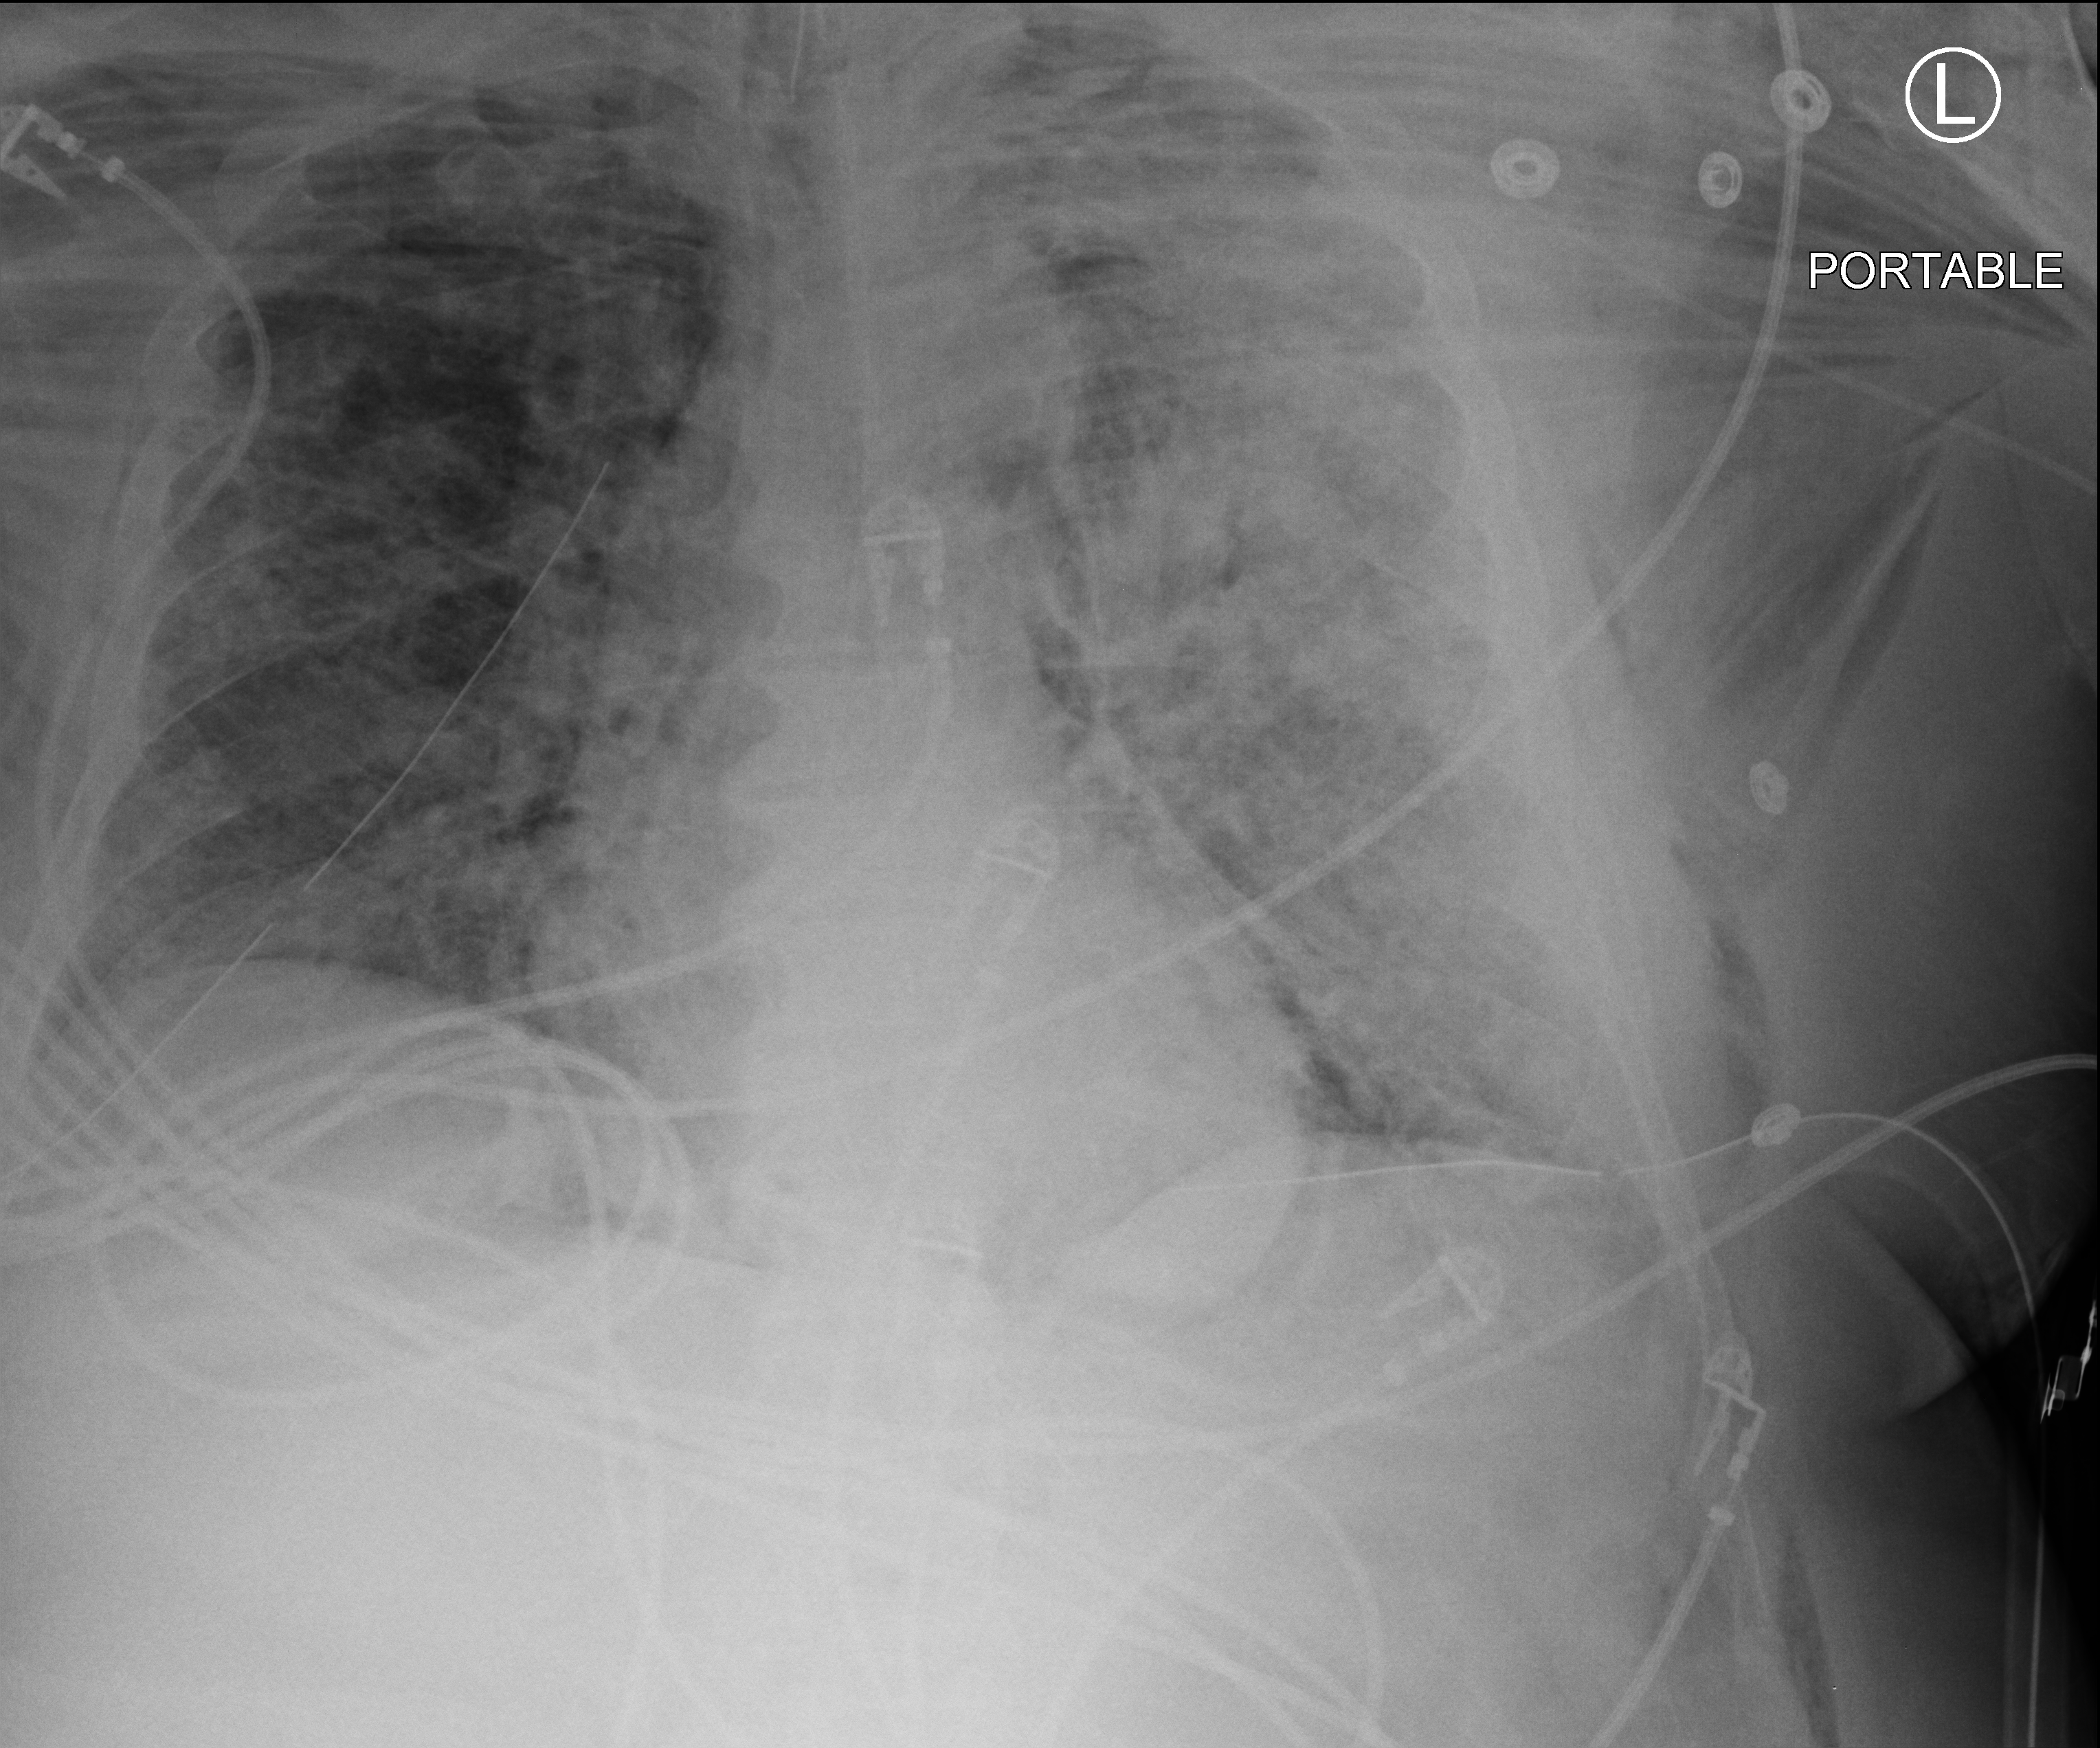
Chest X-ray (portable); anteroposterior (AP) projection. Patient hospitalised with COVID-19, aged 18–59 years.
From the hospital-stay record, not from the radiograph (when in the stay this image was taken is not recorded): admitted to intensive care during this hospital stay: yes.